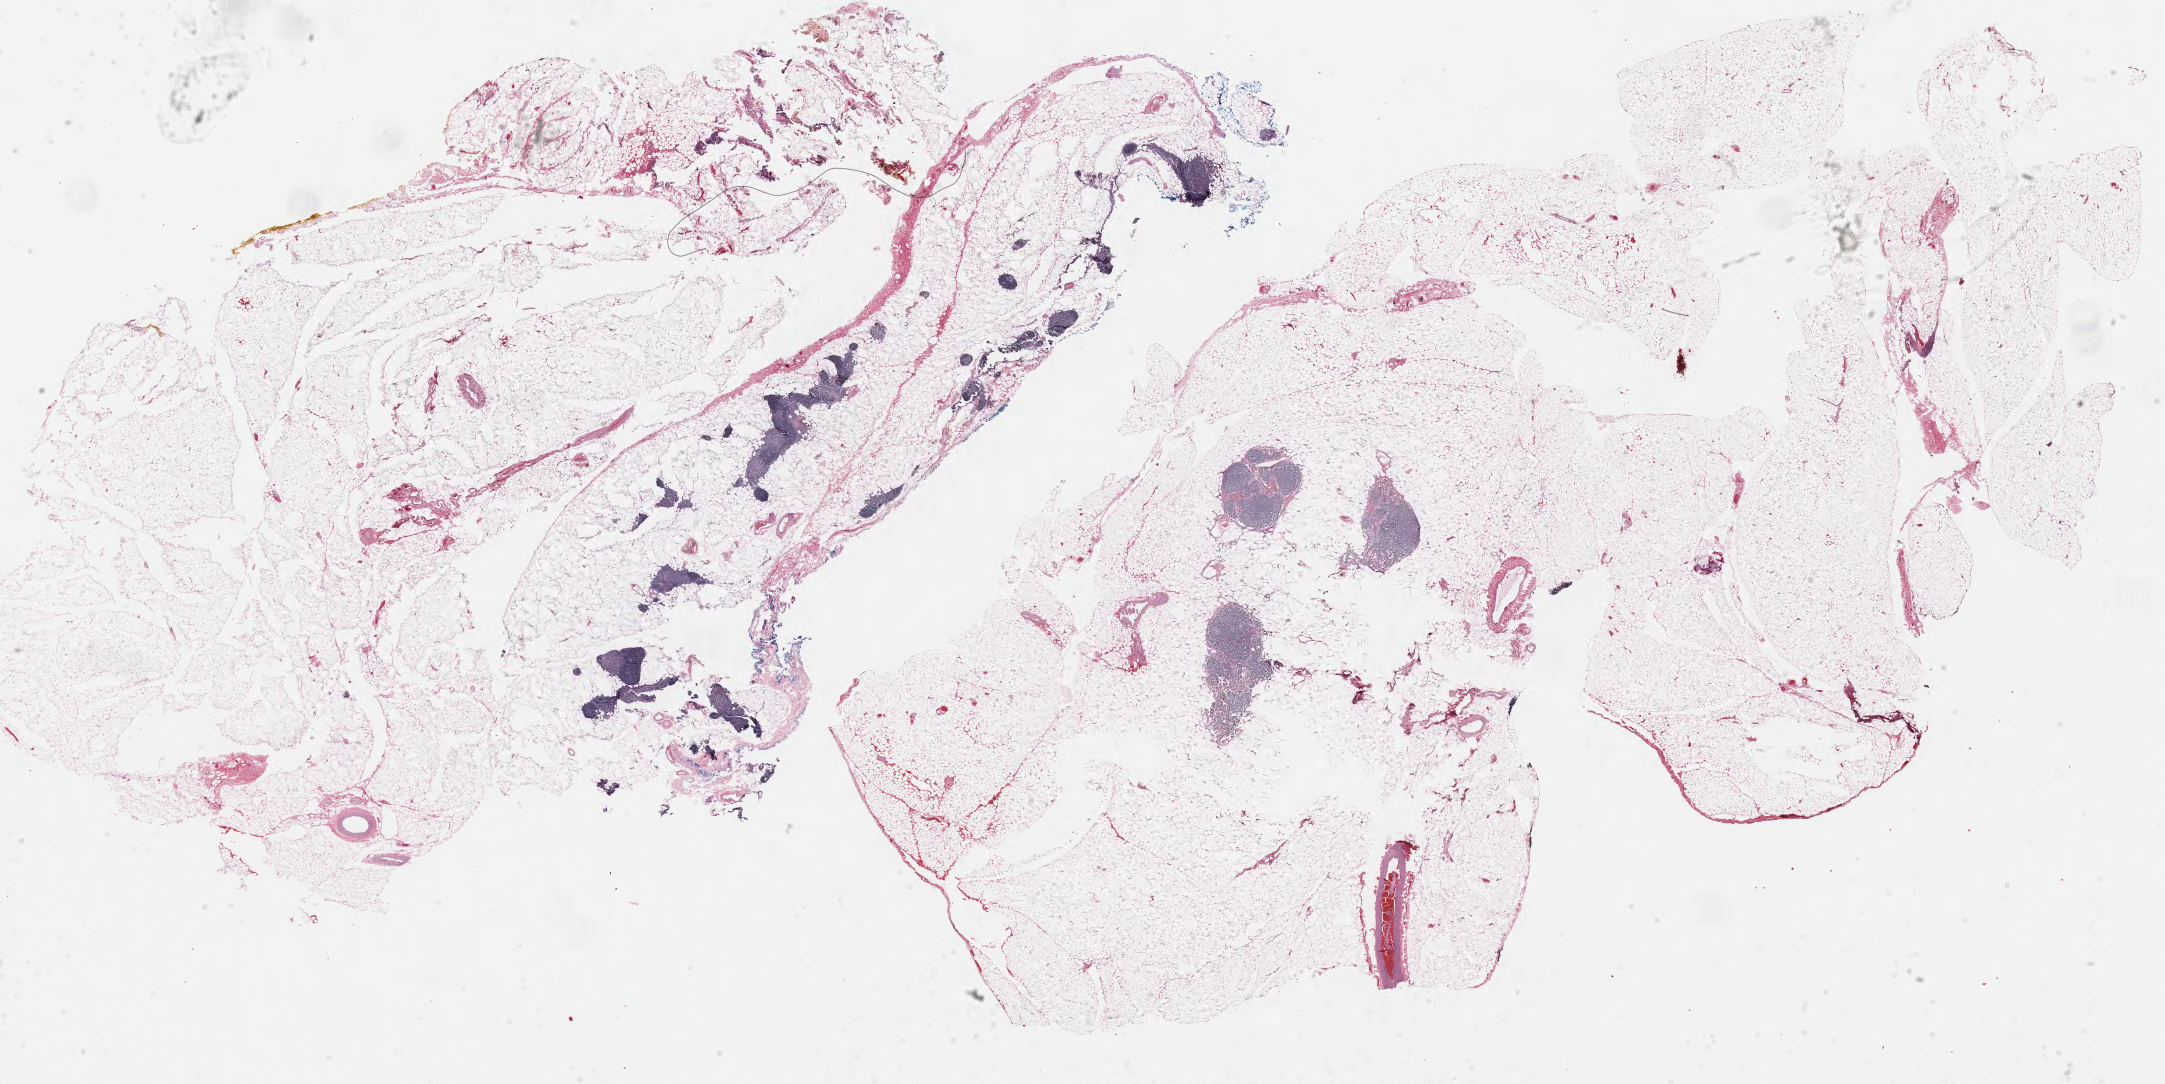
Whole-slide histology image, Hematoxylin and eosin (H&E) stained, shown as a low-resolution overview of the whole scanned area (about 34.3 x 17.2 mm, slide scanned at 40x), FFPE section, thymus, primary tumour sample. Patient: female, age at initial diagnosis 50 years.
Diagnosis: Thymoma, type AB, malignant.